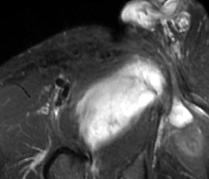
MRI of an extremity soft-tissue mass, one axial slice. Slice 68 of 89 in the series (ordered by position). STIR. MR volume resampled by the dataset authors to the PET/CT grid (not the native acquisition matrix). 3.27 mm slice thickness. 209 × 179 image matrix, field of view 204 × 175 mm. Male patient. Case-level facts recorded for this patient, not image findings: histological type: undifferentiated - pleiomorphic; grade: high; site of the primary tumour: right thigh.
Structures marked on this image (expert contour drawn on MRI and transferred to this co-registered scan by the dataset authors):
- gross tumour volume including surrounding oedema: box from (x=78, y=60) to (x=163, y=147) px
- gross tumour volume (mass): (x=76, y=62)–(x=161, y=147)